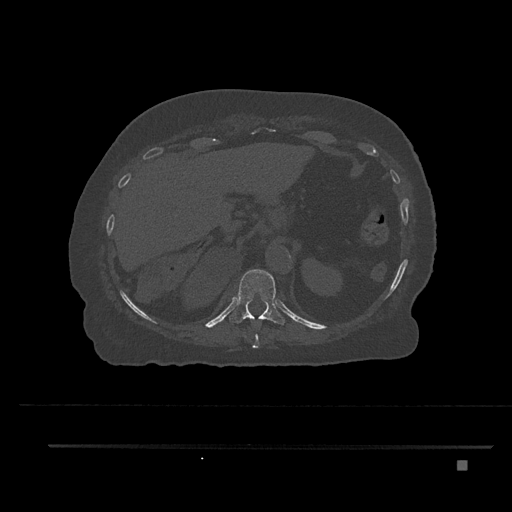
CT including the spine, one axial slice. Slice 318 of 797 in the series (ordered by position). Reconstruction kernel Br40s/3. Bone window (W 1800 / L 400 HU). 0.5 mm slice thickness. 512 × 512 image matrix. Female patient, age 76 years. From the clinical record (not read from this slice): primary cancer: lung; vertebrae with lytic lesions (as recorded): T11, L3.
Outlined on this slice (semi-automatic segmentation, software-assisted and operator-edited):
- T10 vertebra: box from (x=252, y=319) to (x=260, y=348) px
- T11 vertebra: (x=229, y=269)–(x=285, y=325)